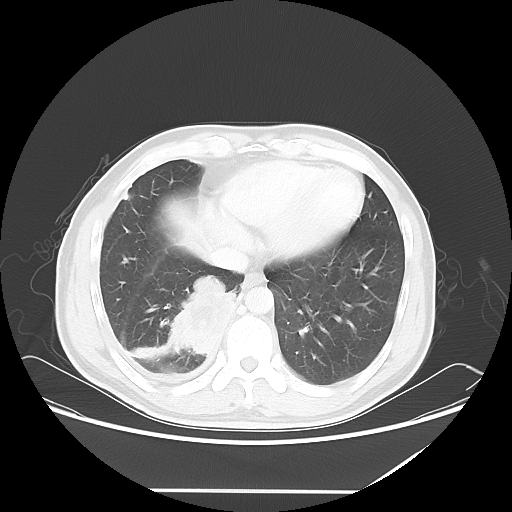
Chest CT, one axial slice. Slice 19 of 60 in the series (ordered by position). Reconstruction kernel LUNG. 120 kVp. Lung window (W 1500 / L -600 HU). 512 × 512 image matrix. Patient: male, 48 years. Case-level facts recorded for this patient, not image findings: clinical TNM (as recorded): T3 N3 M1a.
Structures marked on this image (bounding box drawn by a radiologist):
- lung tumour (recorded histology: squamous cell carcinoma): bounding box [x1, y1, x2, y2] px = [165, 271, 239, 361]